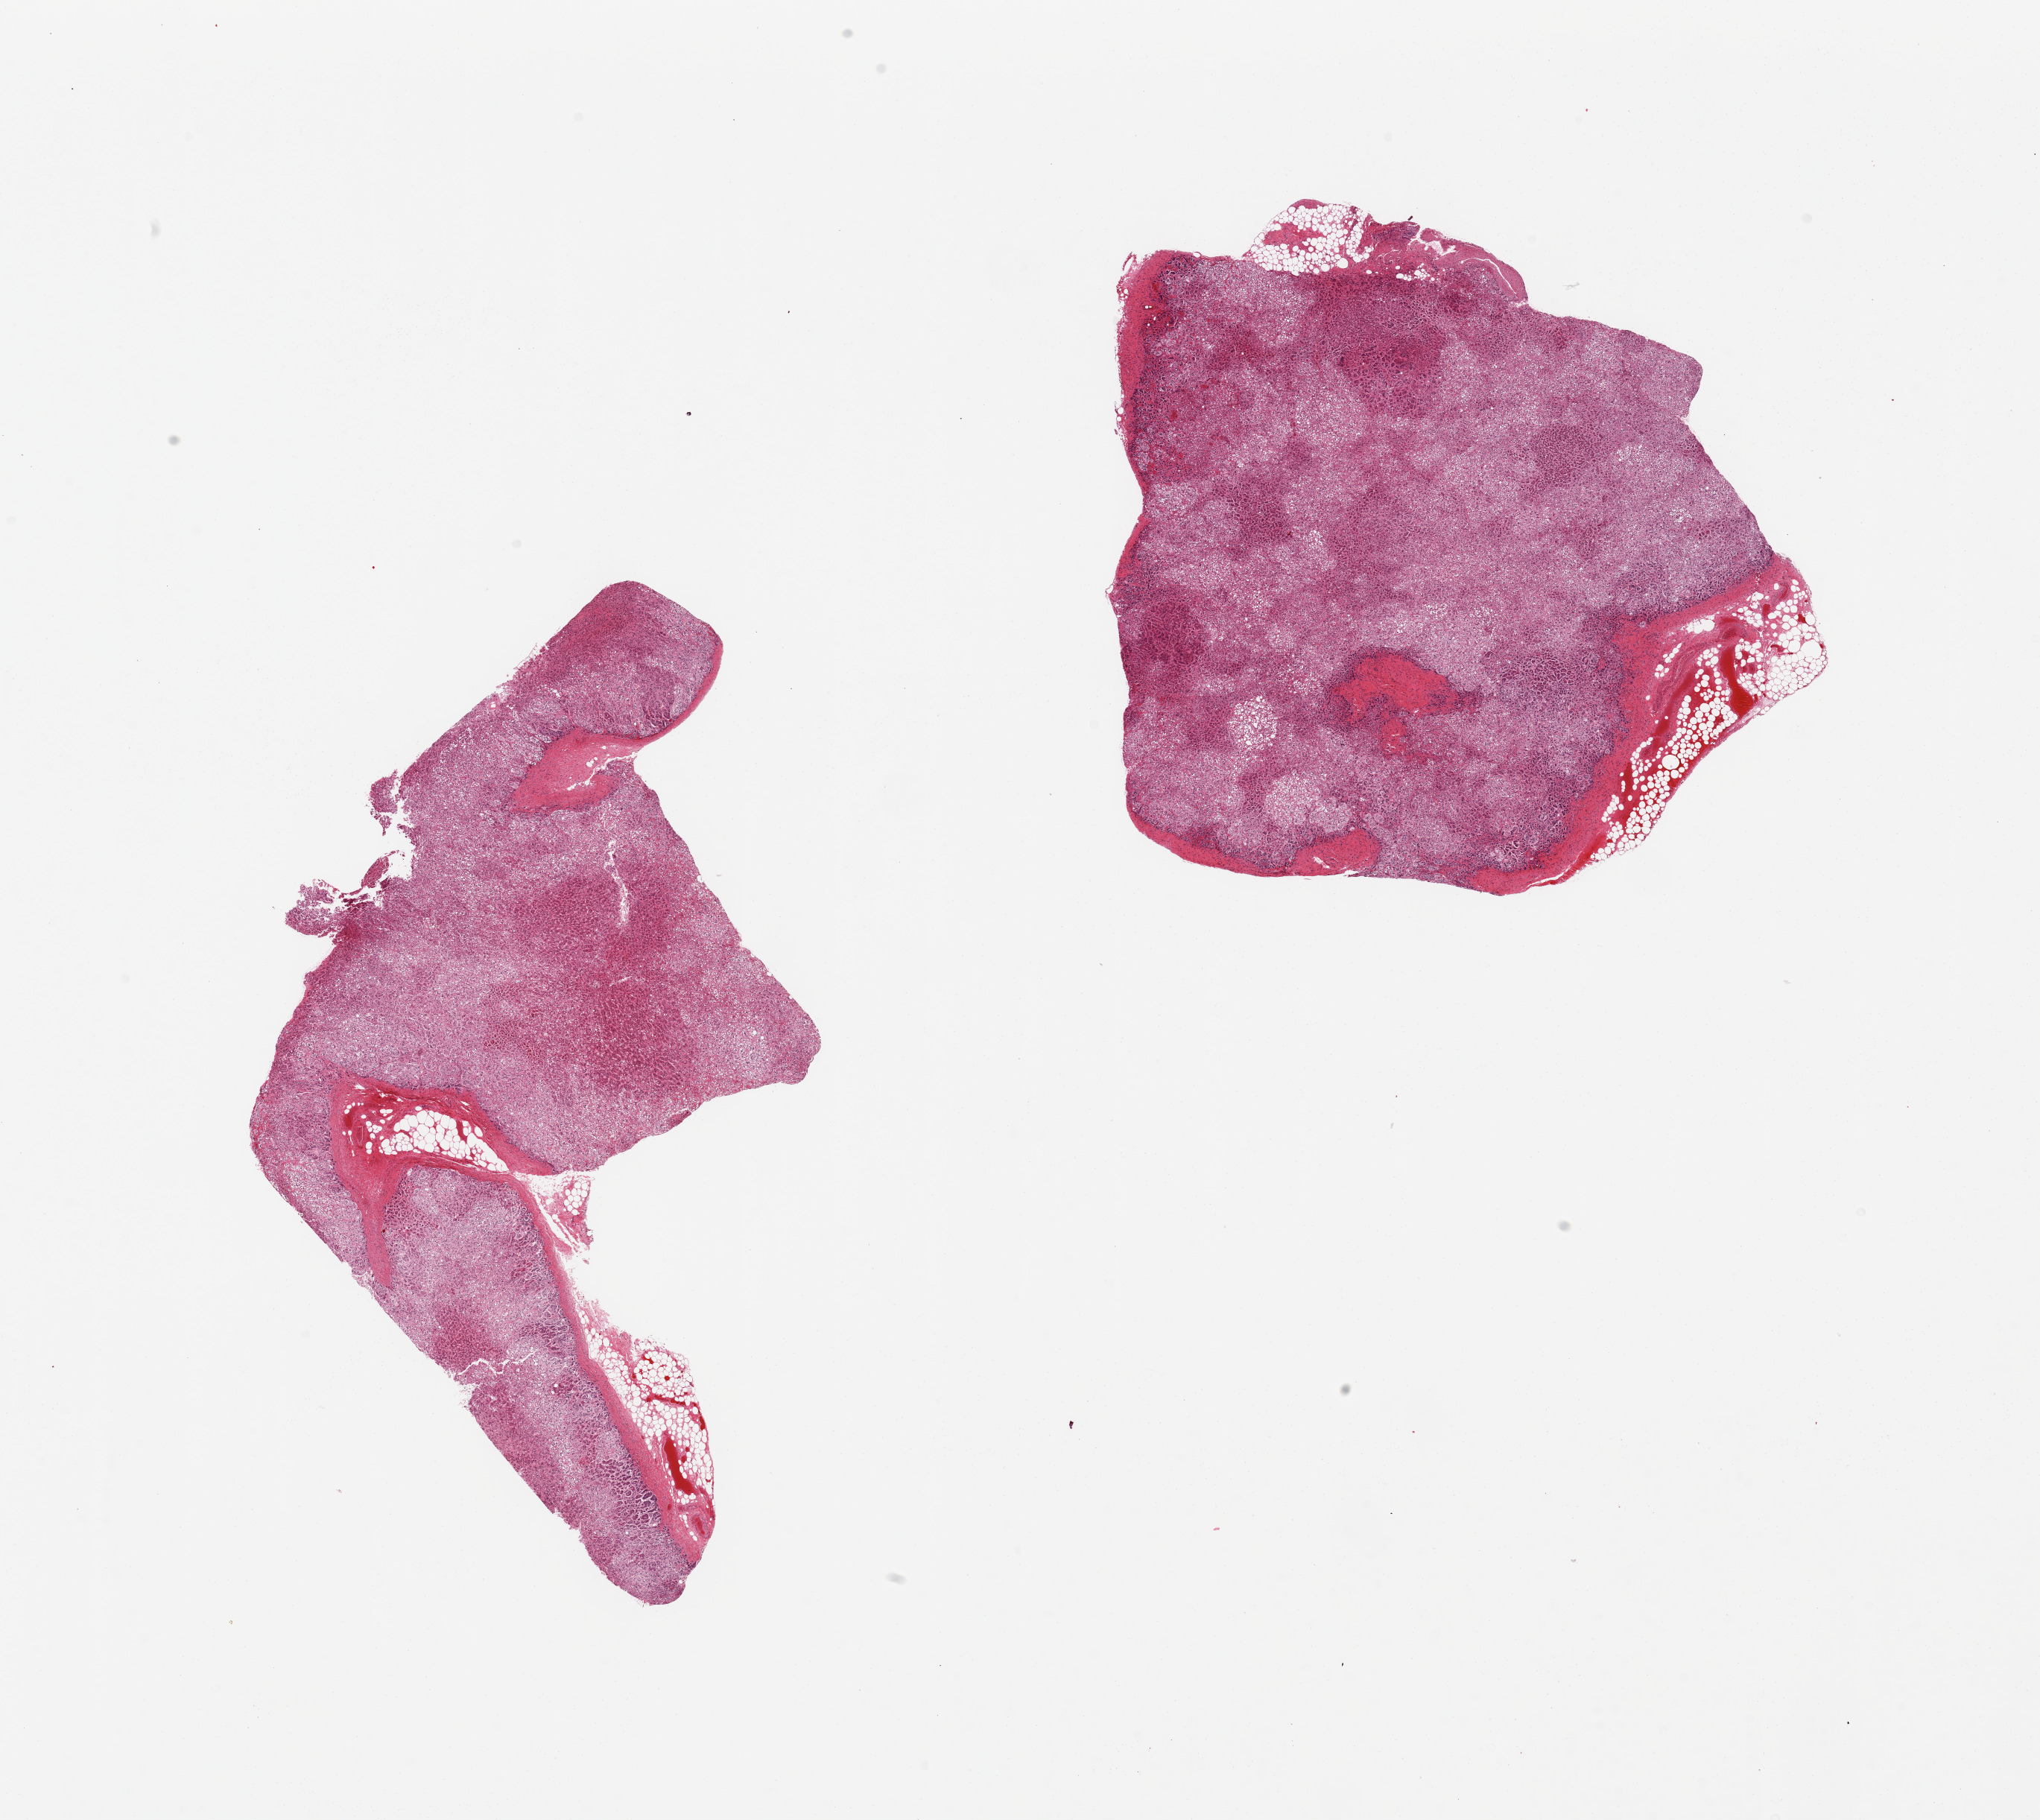
Whole-slide image, haematoxylin and eosin stain, shown as a low-resolution overview of the whole scanned area (about 21.7 x 19.3 mm, acquisition: 20x scan). PAXgene-fixed, paraffin-embedded tissue. Section of adrenal gland (target tissue). Donor tissue sample. Male donor.
Review note (as recorded): 2 pieces; 10% external fat.